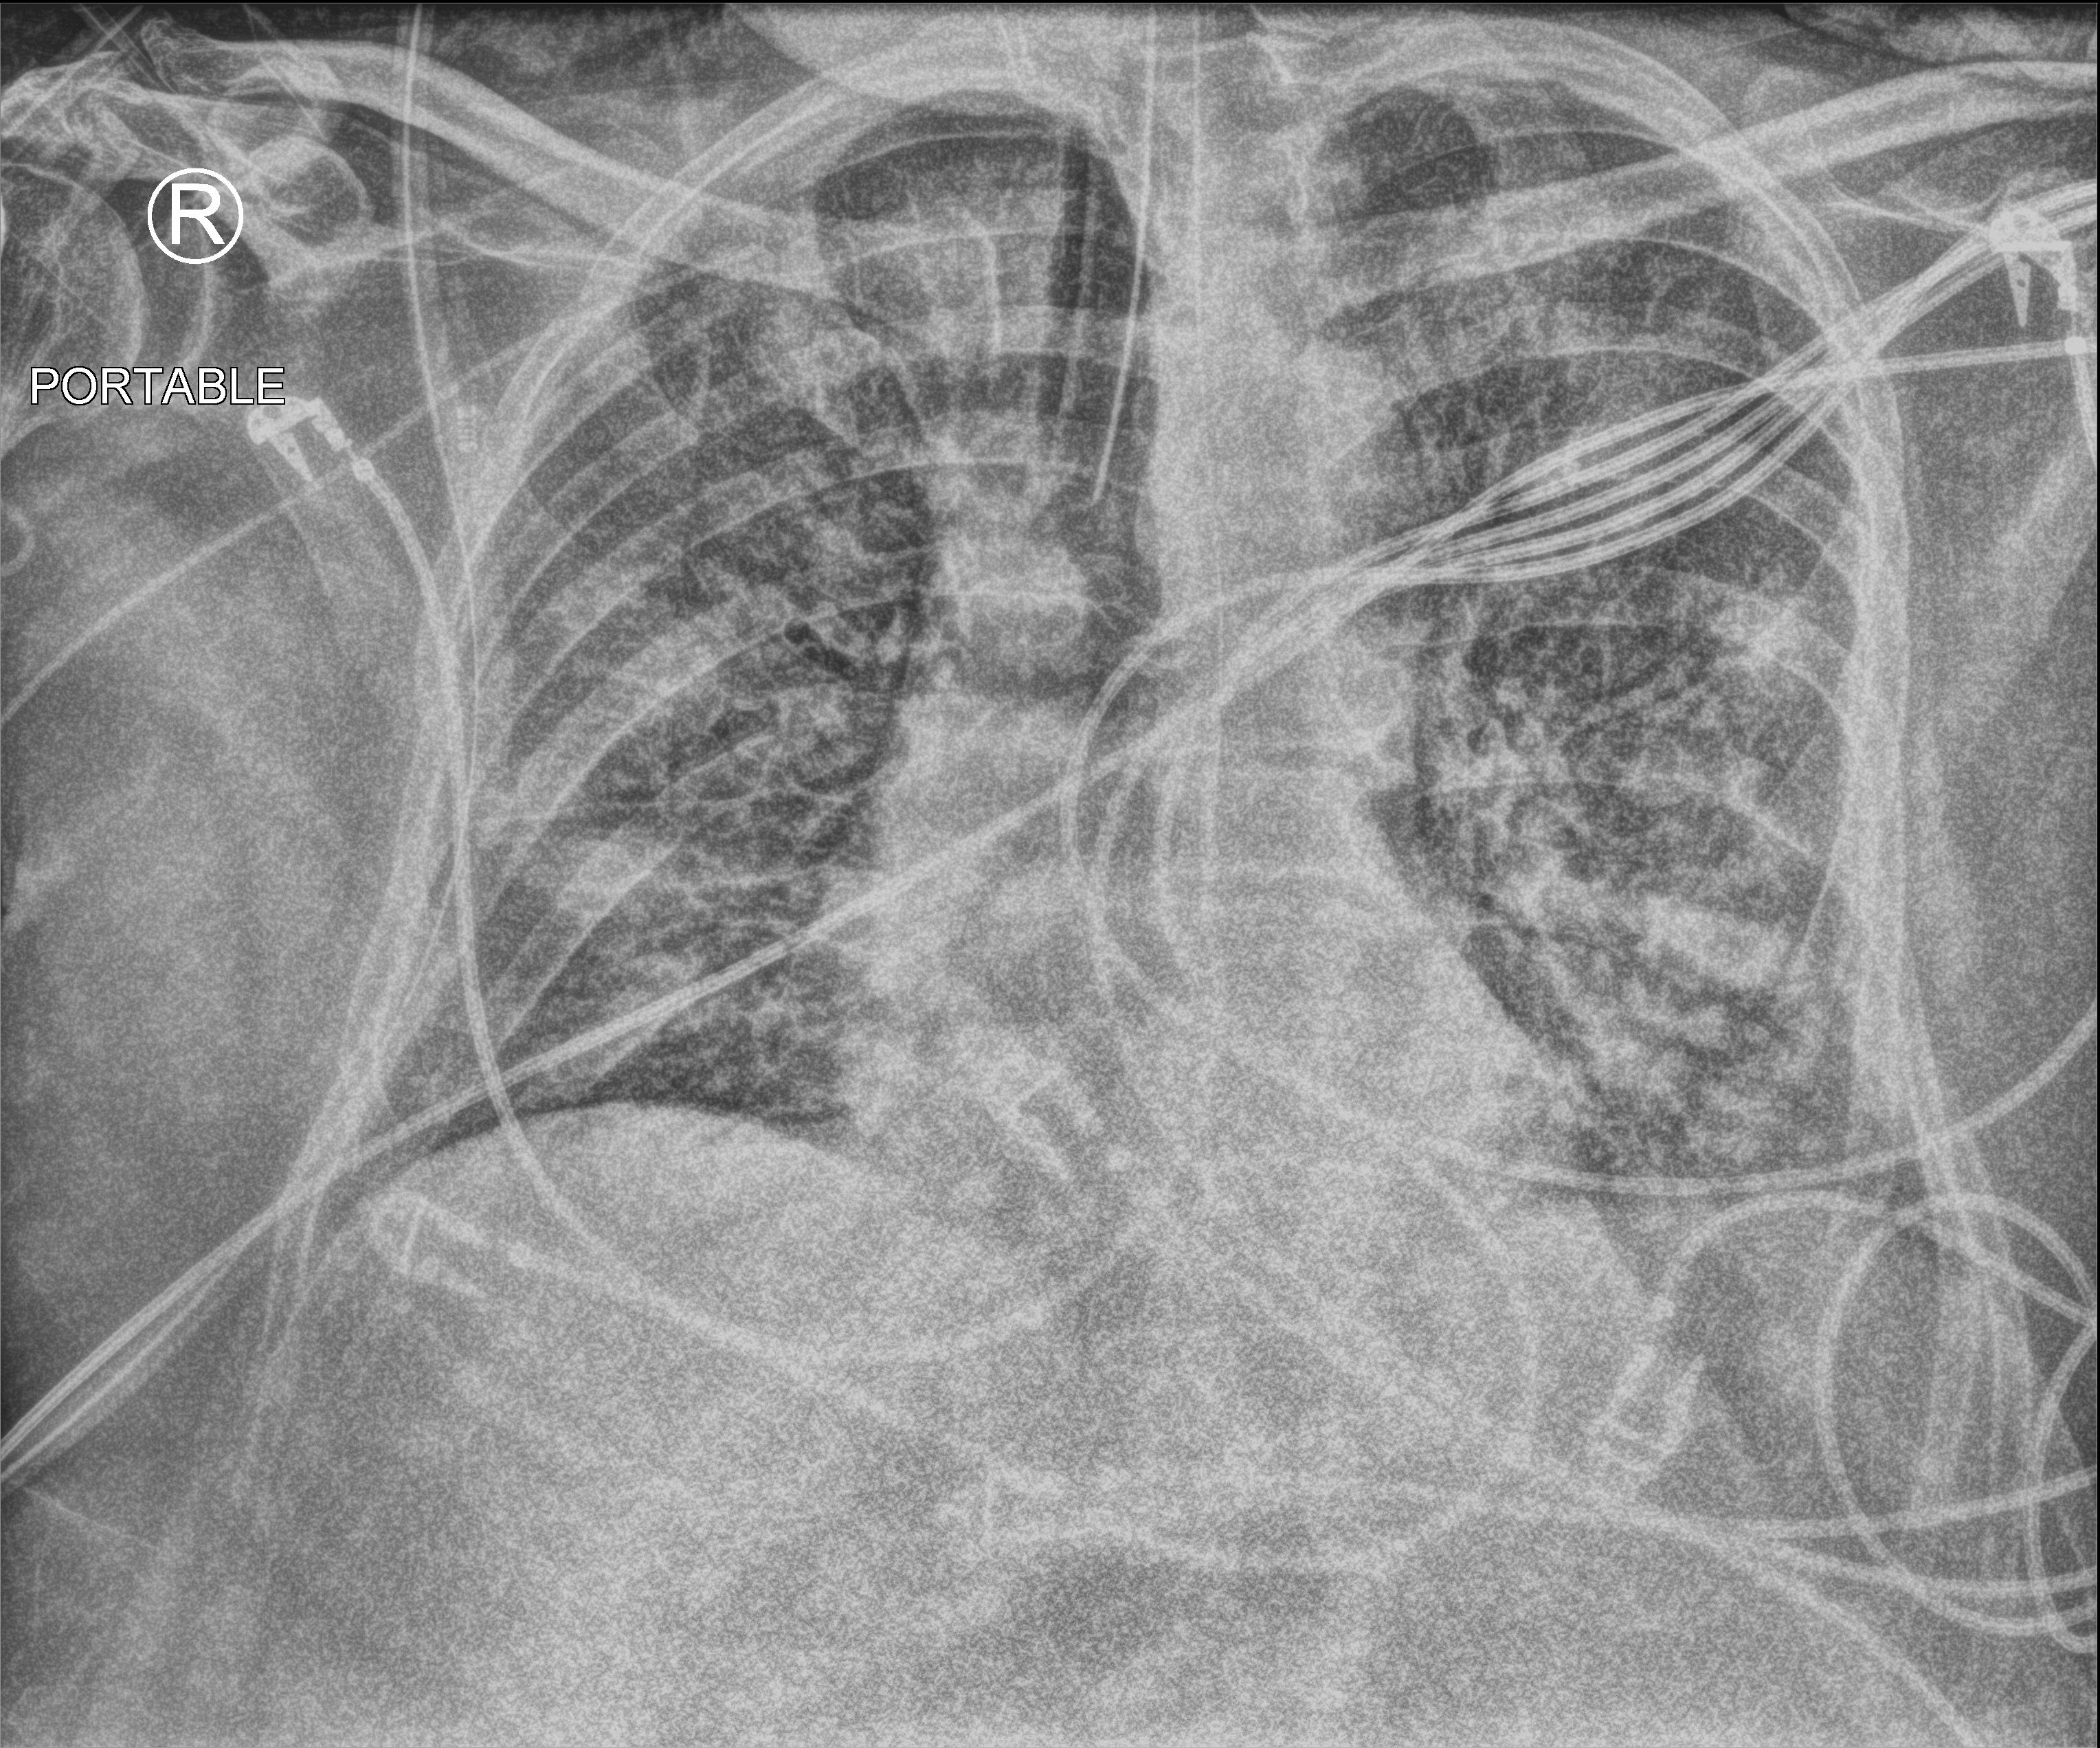
Bedside chest radiograph (computed radiography); anteroposterior (AP) projection. Male patient hospitalised with COVID-19, age 60–74 years.
Admission-level facts for this patient (not findings on this image; timing relative to this image not recorded):
- admitted to intensive care during this hospital stay: yes
- mechanically ventilated during this hospital stay: yes
- length of hospital stay: 20 days